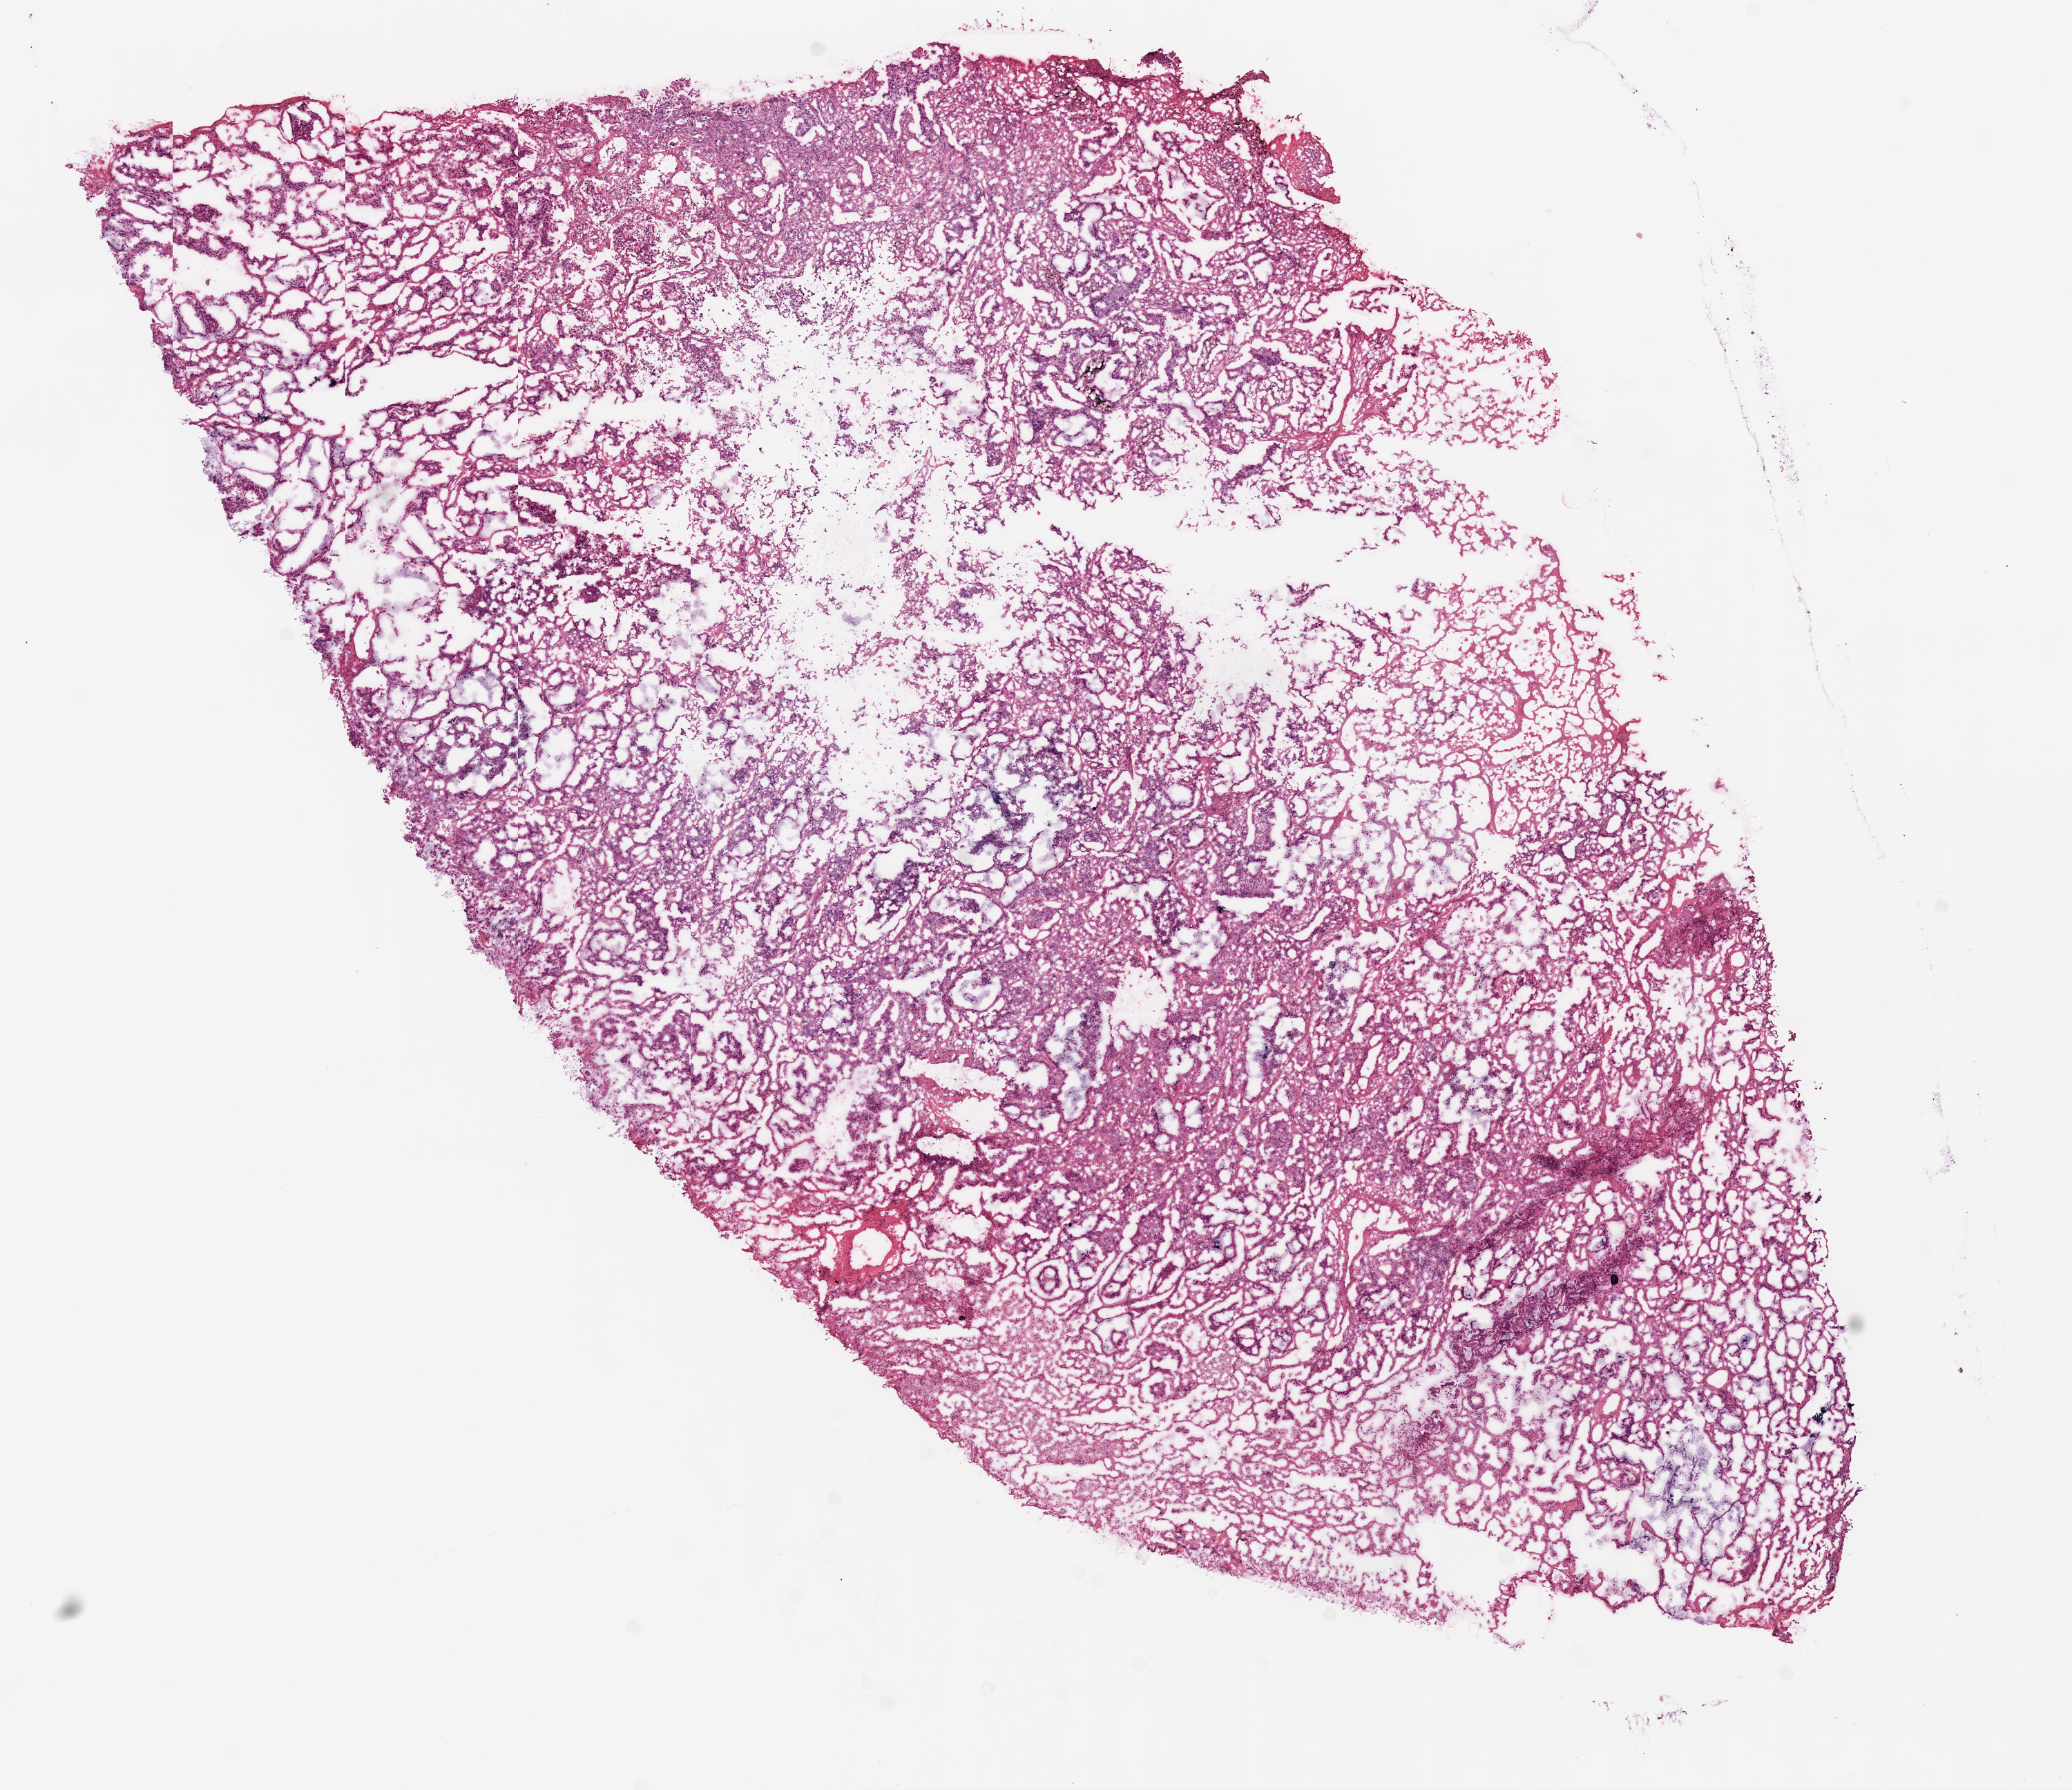
Hematoxylin and eosin (H&E) stained whole-slide image, low-resolution overview of the scanned area, about 12.0 x 10.4 mm (from a 20x scan); frozen section; primary tumour sample from the lung. Male patient; age at initial diagnosis 77 years. Pathologist review of this section (percent, as recorded): tumour cells 70%, tumour nuclei 70%, normal cells 20%, stromal cells 5%, necrosis 5%.
AJCC pathologic stage: IIIA (4th edition). Pathologic diagnosis: Adenocarcinoma, NOS (upper lobe, lung). TNM: T3 N2 M0.